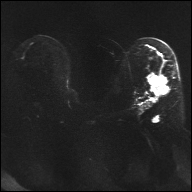
Breast MRI, one axial slice. Slice 19 of 32 in the series (ordered by position). Diffusion-weighted series; image 2 of 4 stored at this slice position (different b-values; order by instance number). 1.5 T. 192 × 192 image matrix, field of view 360 × 360 mm. Female patient.
Structures marked on this image (manually delineated by an expert):
- tumour on diffusion-weighted imaging: bounding box [x1, y1, x2, y2] px = [149, 75, 169, 95]